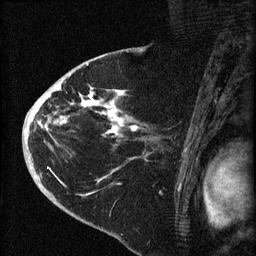
Breast MRI (dynamic contrast-enhanced), one sagittal slice; slice 43 of 60 in the series (ordered by position); dynamic contrast-enhanced series, image 2 of 4 at this slice position (ordered by acquisition); 1.5 T; TE 4.2 ms, TR 8.2 ms; 256 × 256 image matrix, field of view 180 × 180 mm. Female patient, age 71 years.
Structures marked on this image (semi-automatic segmentation, software-assisted and operator-edited):
- analysis volume of interest (the breast-tissue region the enhancement analysis was run in; not a lesion): bounding box <35,75,153,190> (left, top, right, bottom; pixels)
- tumour enhancement mask (voxels above the 70 % enhancement threshold inside the analysis volume of interest): <35,82,139,182>